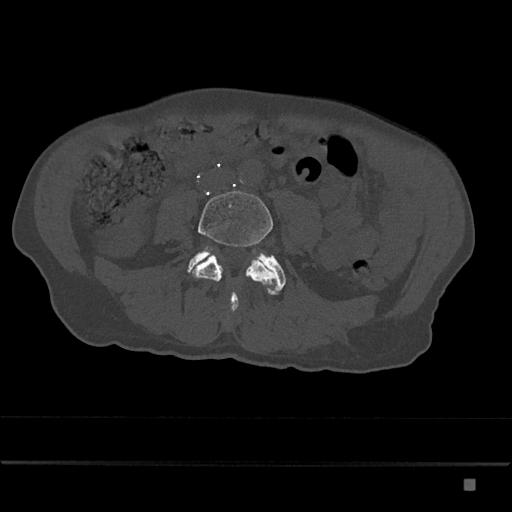
CT including the spine, one axial slice; slice 321 of 797 in the series (ordered by position); 120 kVp; bone window (W 1800 / L 400 HU); 0.5 mm slice thickness; 512 × 512 image matrix. Male patient, age 72 years. Case-level facts recorded for this patient, not image findings: primary cancer: prostate.
Outlined on this slice (semi-automatic segmentation, software-assisted and operator-edited):
- L4 vertebra: bounding box [x1, y1, x2, y2] px = [188, 191, 277, 311]
- L5 vertebra: [187, 247, 286, 301]